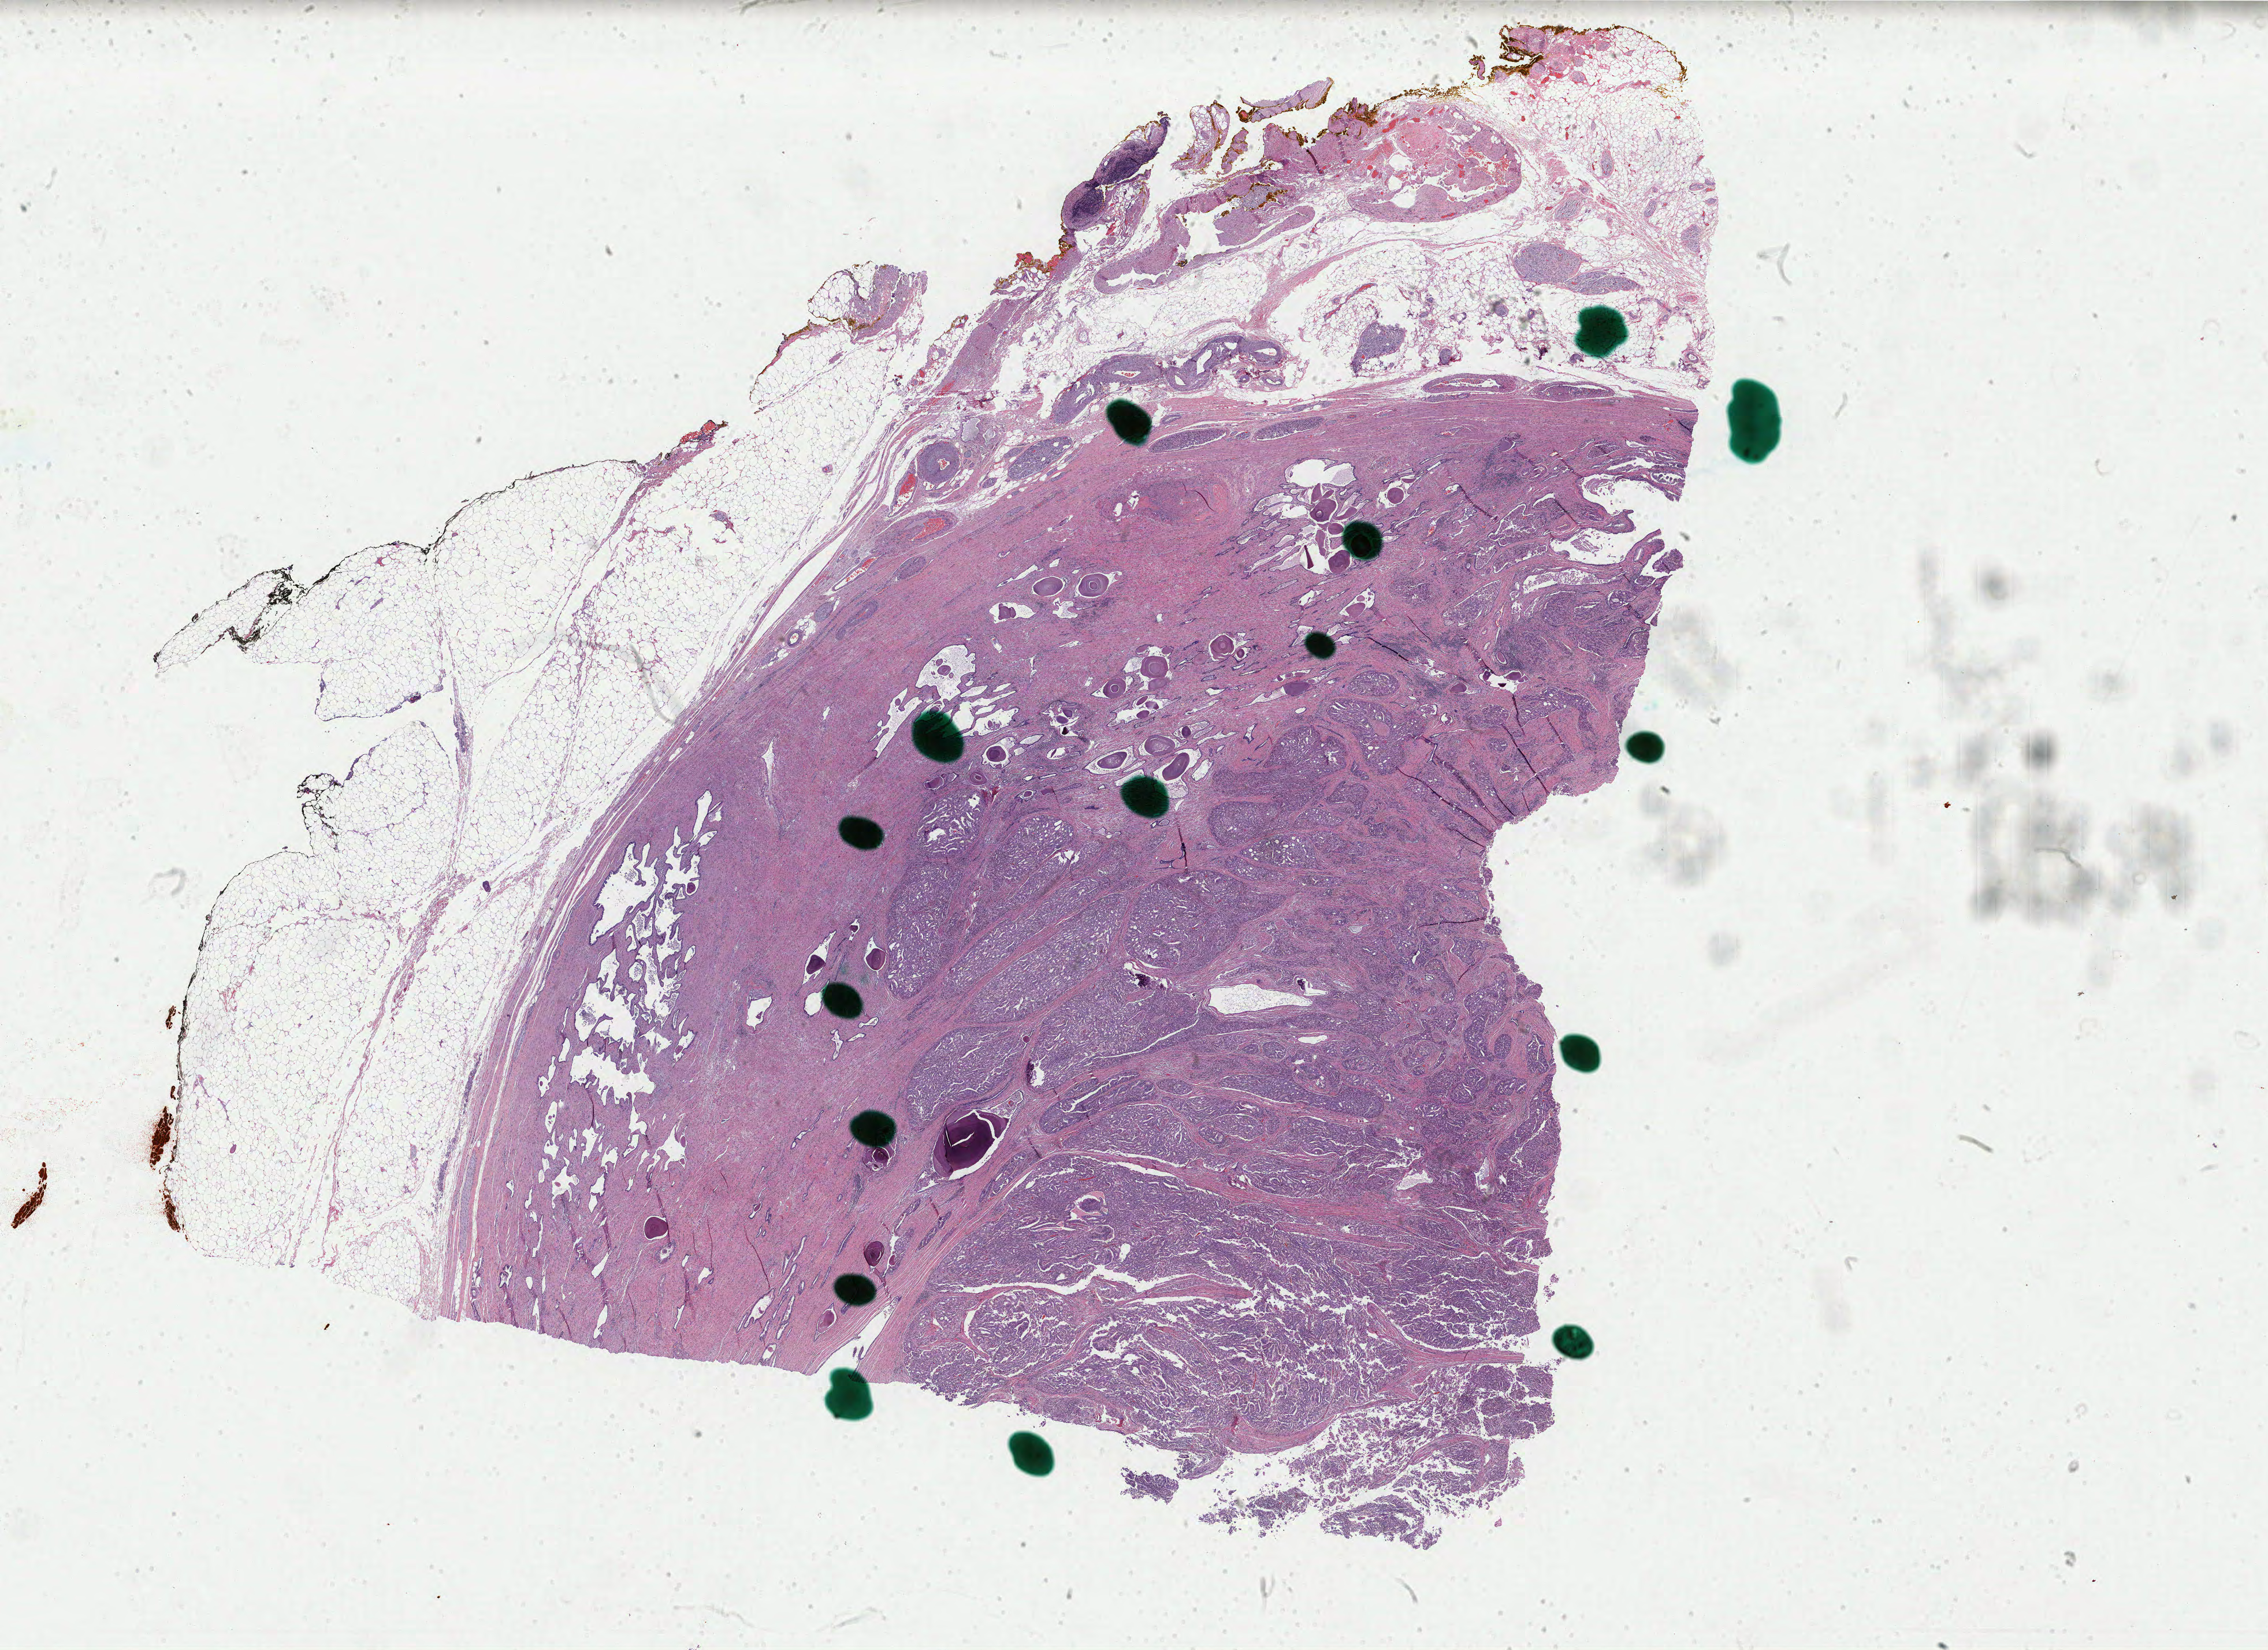
Digitized H&E tissue section (whole slide), a low-resolution overview of the entire scanned area, about 31.2 x 22.7 mm. FFPE section. Primary tumour sample from the prostate. Male, age 65 years at initial diagnosis. Gleason score: 9 (4+5).
Diagnosis: Adenocarcinoma, NOS (prostate gland).